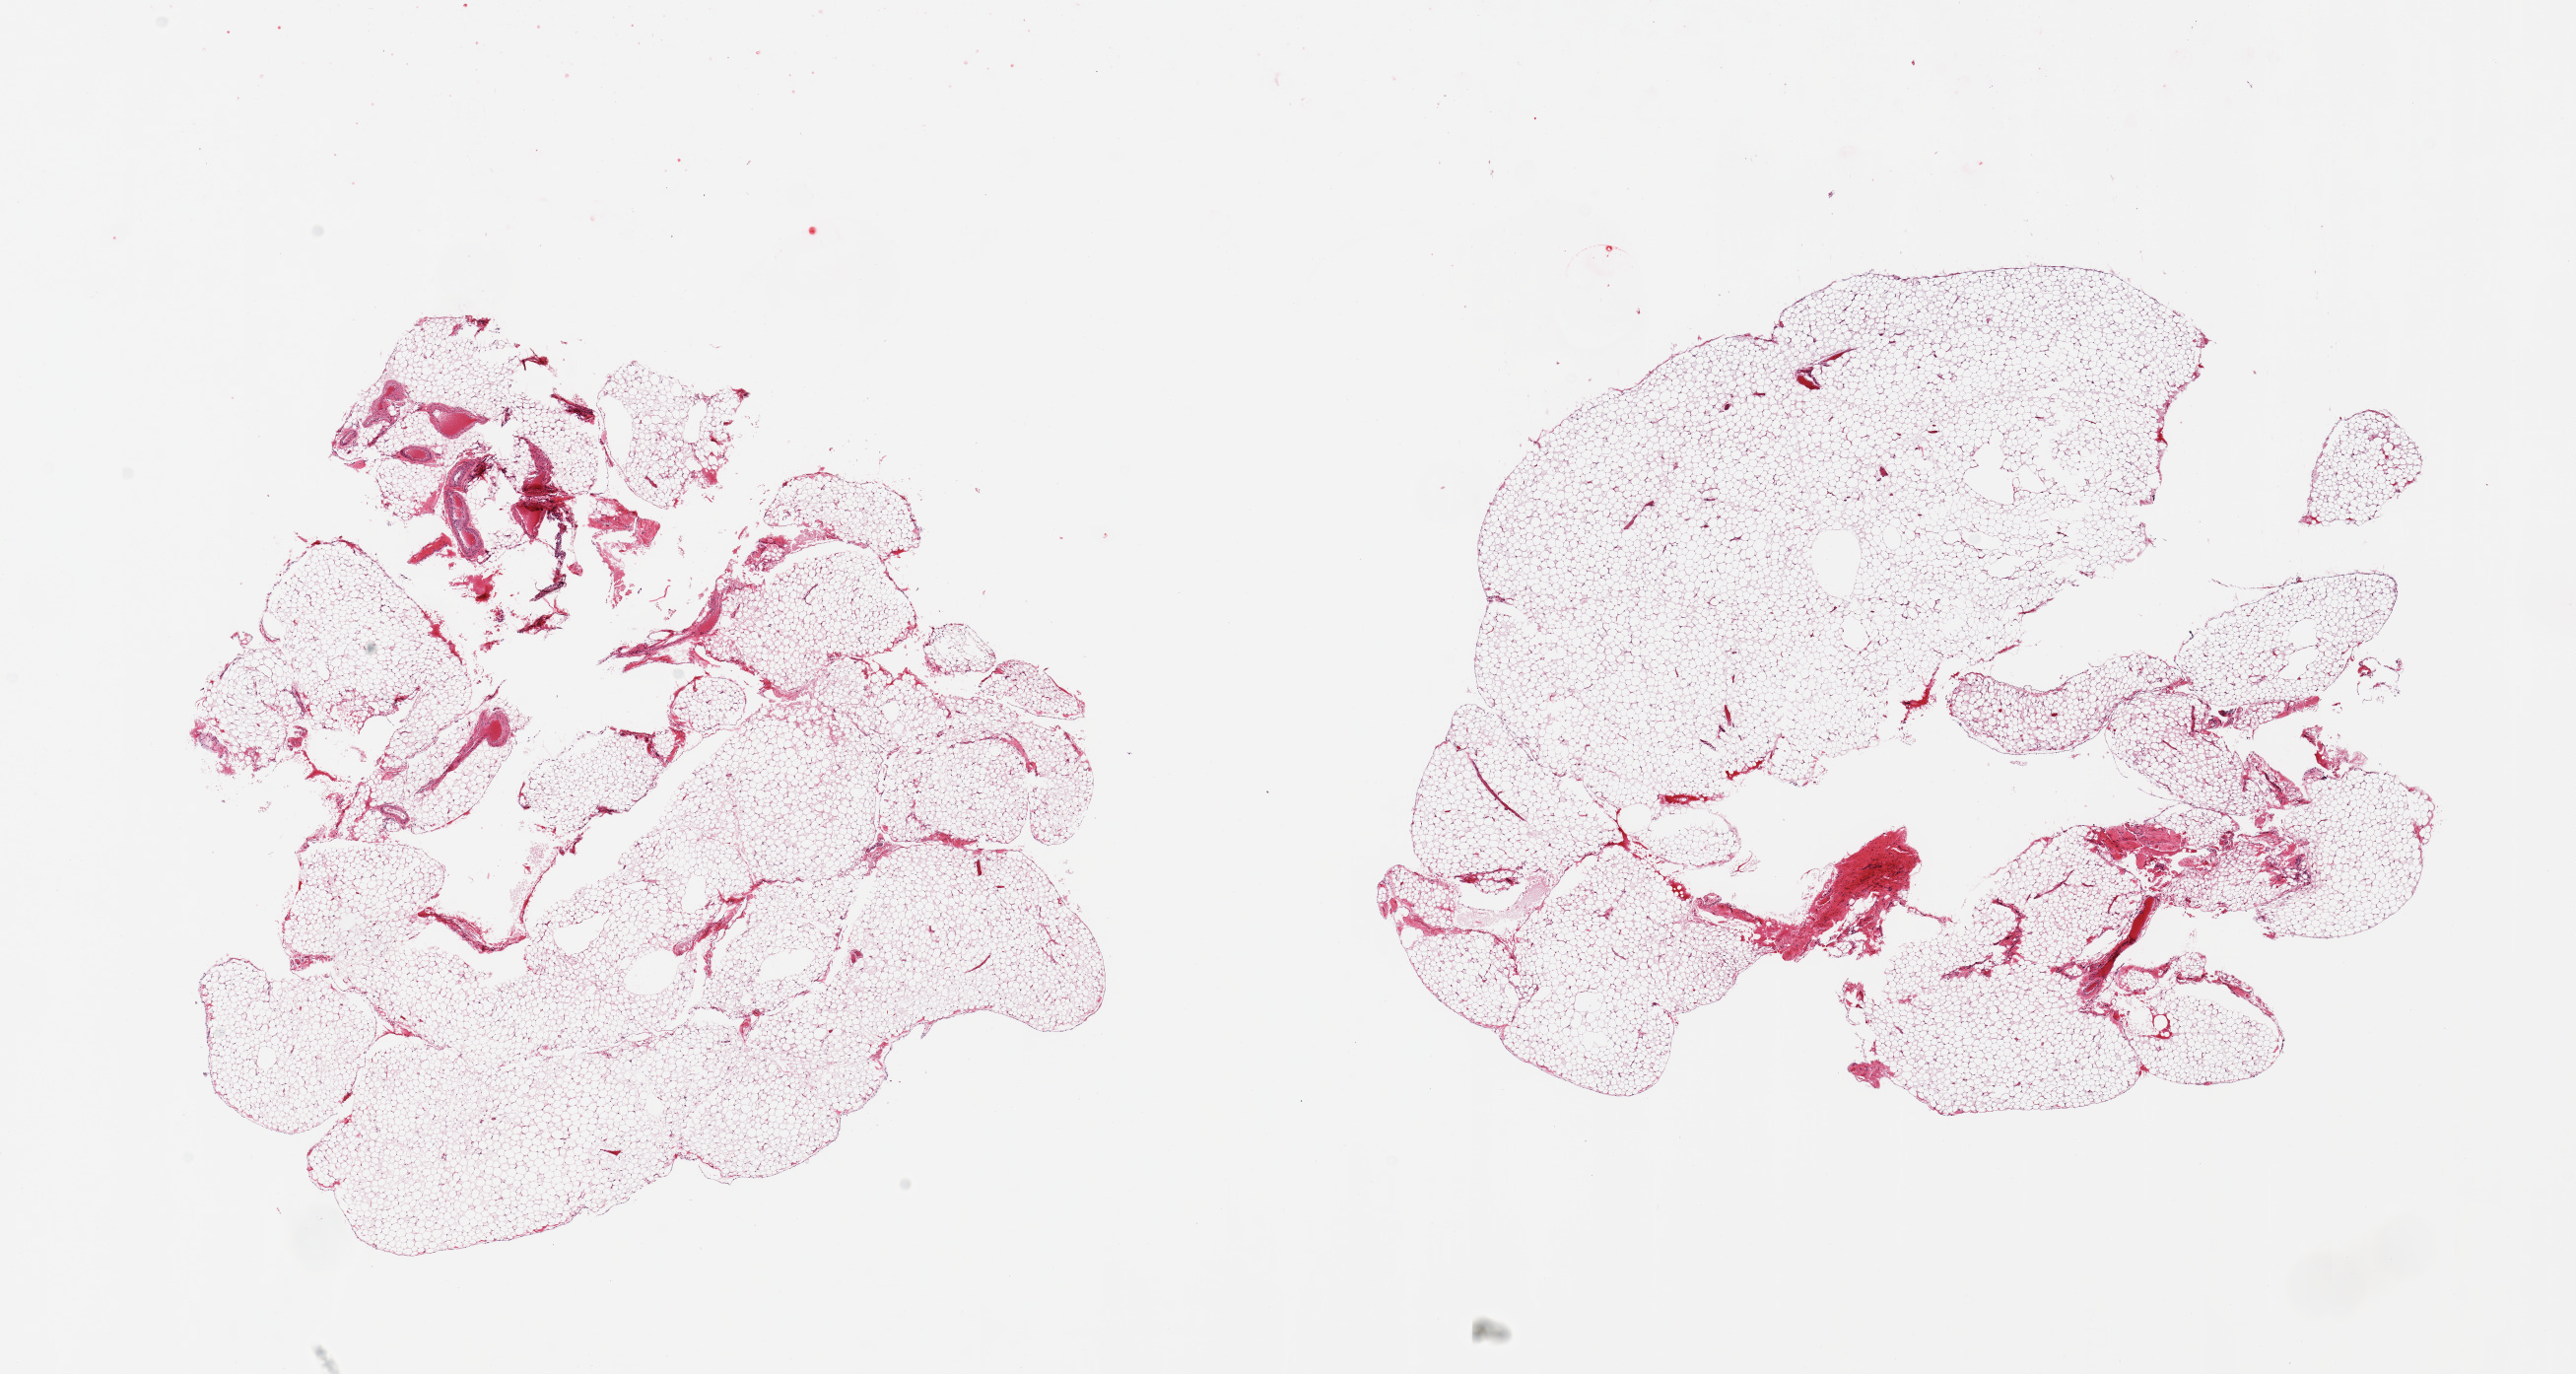
Whole-slide image, hematoxylin and eosin (H&E) stain, whole scanned area (about 20.7 x 11.0 mm, slide scanned at 20x) shown as a low-resolution overview. PAXgene-fixed, paraffin-embedded tissue. Sampled site (target tissue): omentum. Tissue donor sample. Female donor.
Pathologist's review note for this sample: 2 pieces; <5% fat content.